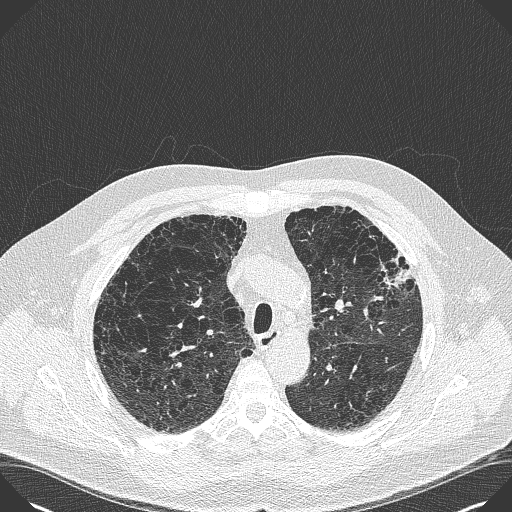
Axial slice from a low-dose chest CT screening exam; baseline screening round; lung window (W 1500 / L -600 HU); lung (sharp) reconstruction kernel (B50f); 120 kVp; slice 116 of 383 in the series. Male participant, aged 59 years at enrolment. Current smoker at enrolment.
- Expert reader's lesion annotation, bounding box <374,245,428,296> (left, top, right, bottom; pixels).
- Screening reader's record for this exam: no non-calcified nodule ≥4 mm recorded.
- Lung cancer was diagnosed 909 days after this screen (after the third annual screen): bronchiolo-alveolar carcinoma, mixed mucinous and non-mucinous, left upper lobe, stage IA (AJCC 6th edition), 20 mm at pathology.